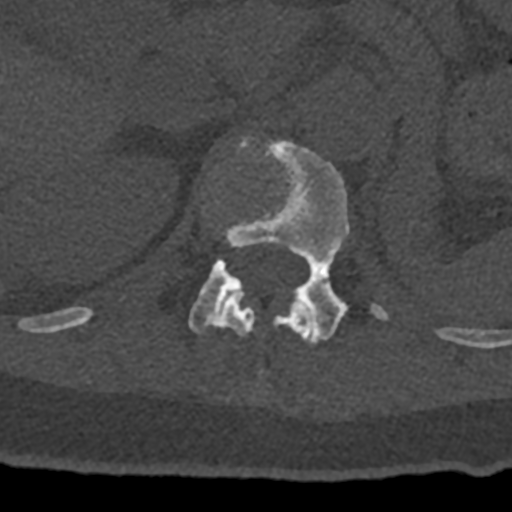
CT including the spine, one axial slice; position 458 of 797 along the scan axis; reconstruction kernel Br40s/3; 120 kVp; bone window (W 1800 / L 400 HU); 0.5 mm slice thickness; 512 × 512 image matrix, field of view 160 × 160 mm. Patient: male, 74 years. From the clinical record (not read from this slice): primary cancer: renal; vertebrae with lytic lesions (as recorded): T10, L1, L2, L3, L4, L5.
Annotated regions visible in this slice (semi-automatic segmentation, software-assisted and operator-edited):
- L1 vertebra: box from (x=189, y=136) to (x=389, y=343) px
- T12 vertebra: (x=70, y=296)–(x=313, y=344)